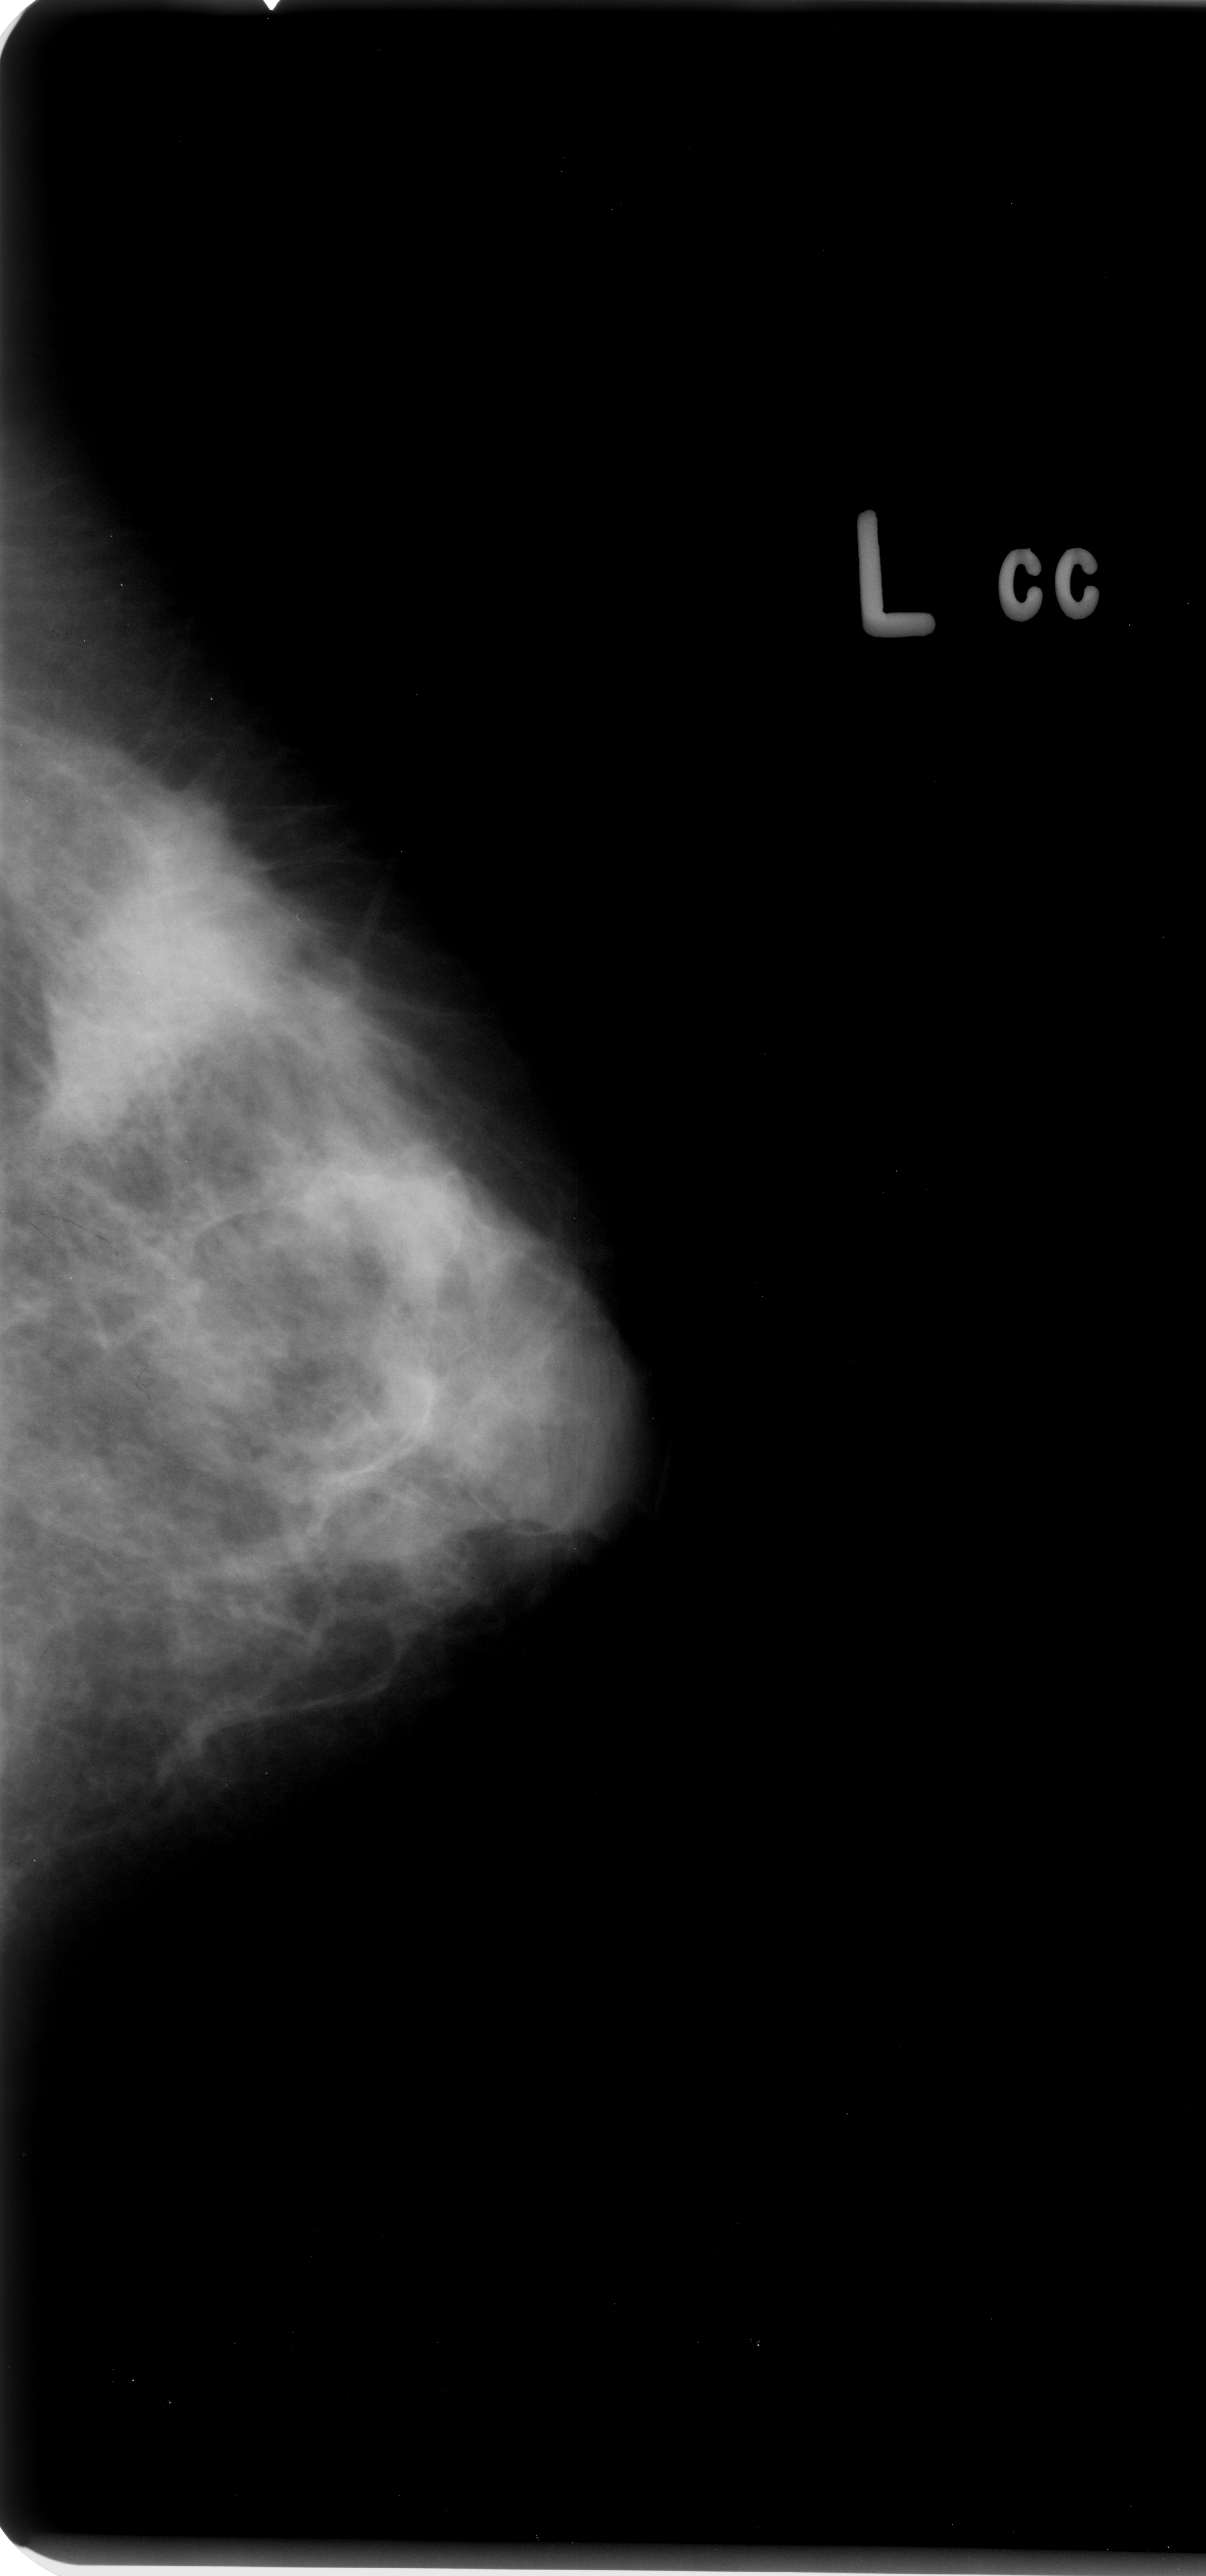
Digitized screen-film mammogram, left breast, CC view, breast composition: heterogeneously dense (BI-RADS density category 3 of 4).
- Marked findings (only marked abnormalities are described; nothing is implied about the rest of the image): calcifications, morphology amorphous / round and regular, distribution clustered; BI-RADS assessment category 4; subtlety rating 4 on a 1 (subtle) to 5 (obvious) scale; pathology (as recorded): malignant.